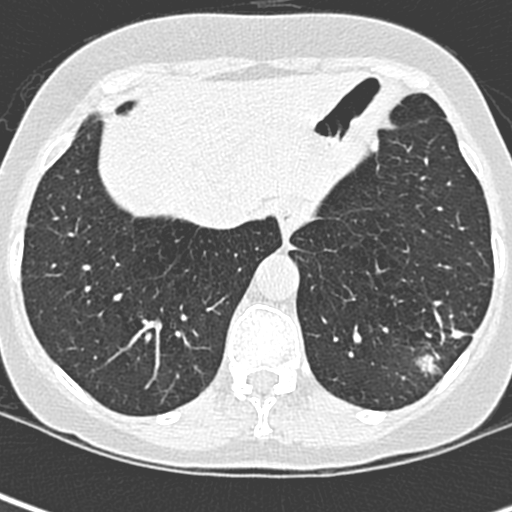
Low-dose screening chest CT, one axial slice; slice 68 of 252 in the series (ordered by position); 120 kVp; lung window (W 1500 / L -600 HU); 1.3 mm slice thickness; 512 × 512 image matrix, field of view 271 × 271 mm.
Annotated regions visible in this slice (outlined manually by an expert reader):
- lesion 1 (tumor, lower lobe of left lung): bounding box <416,326,467,376> (left, top, right, bottom; pixels)